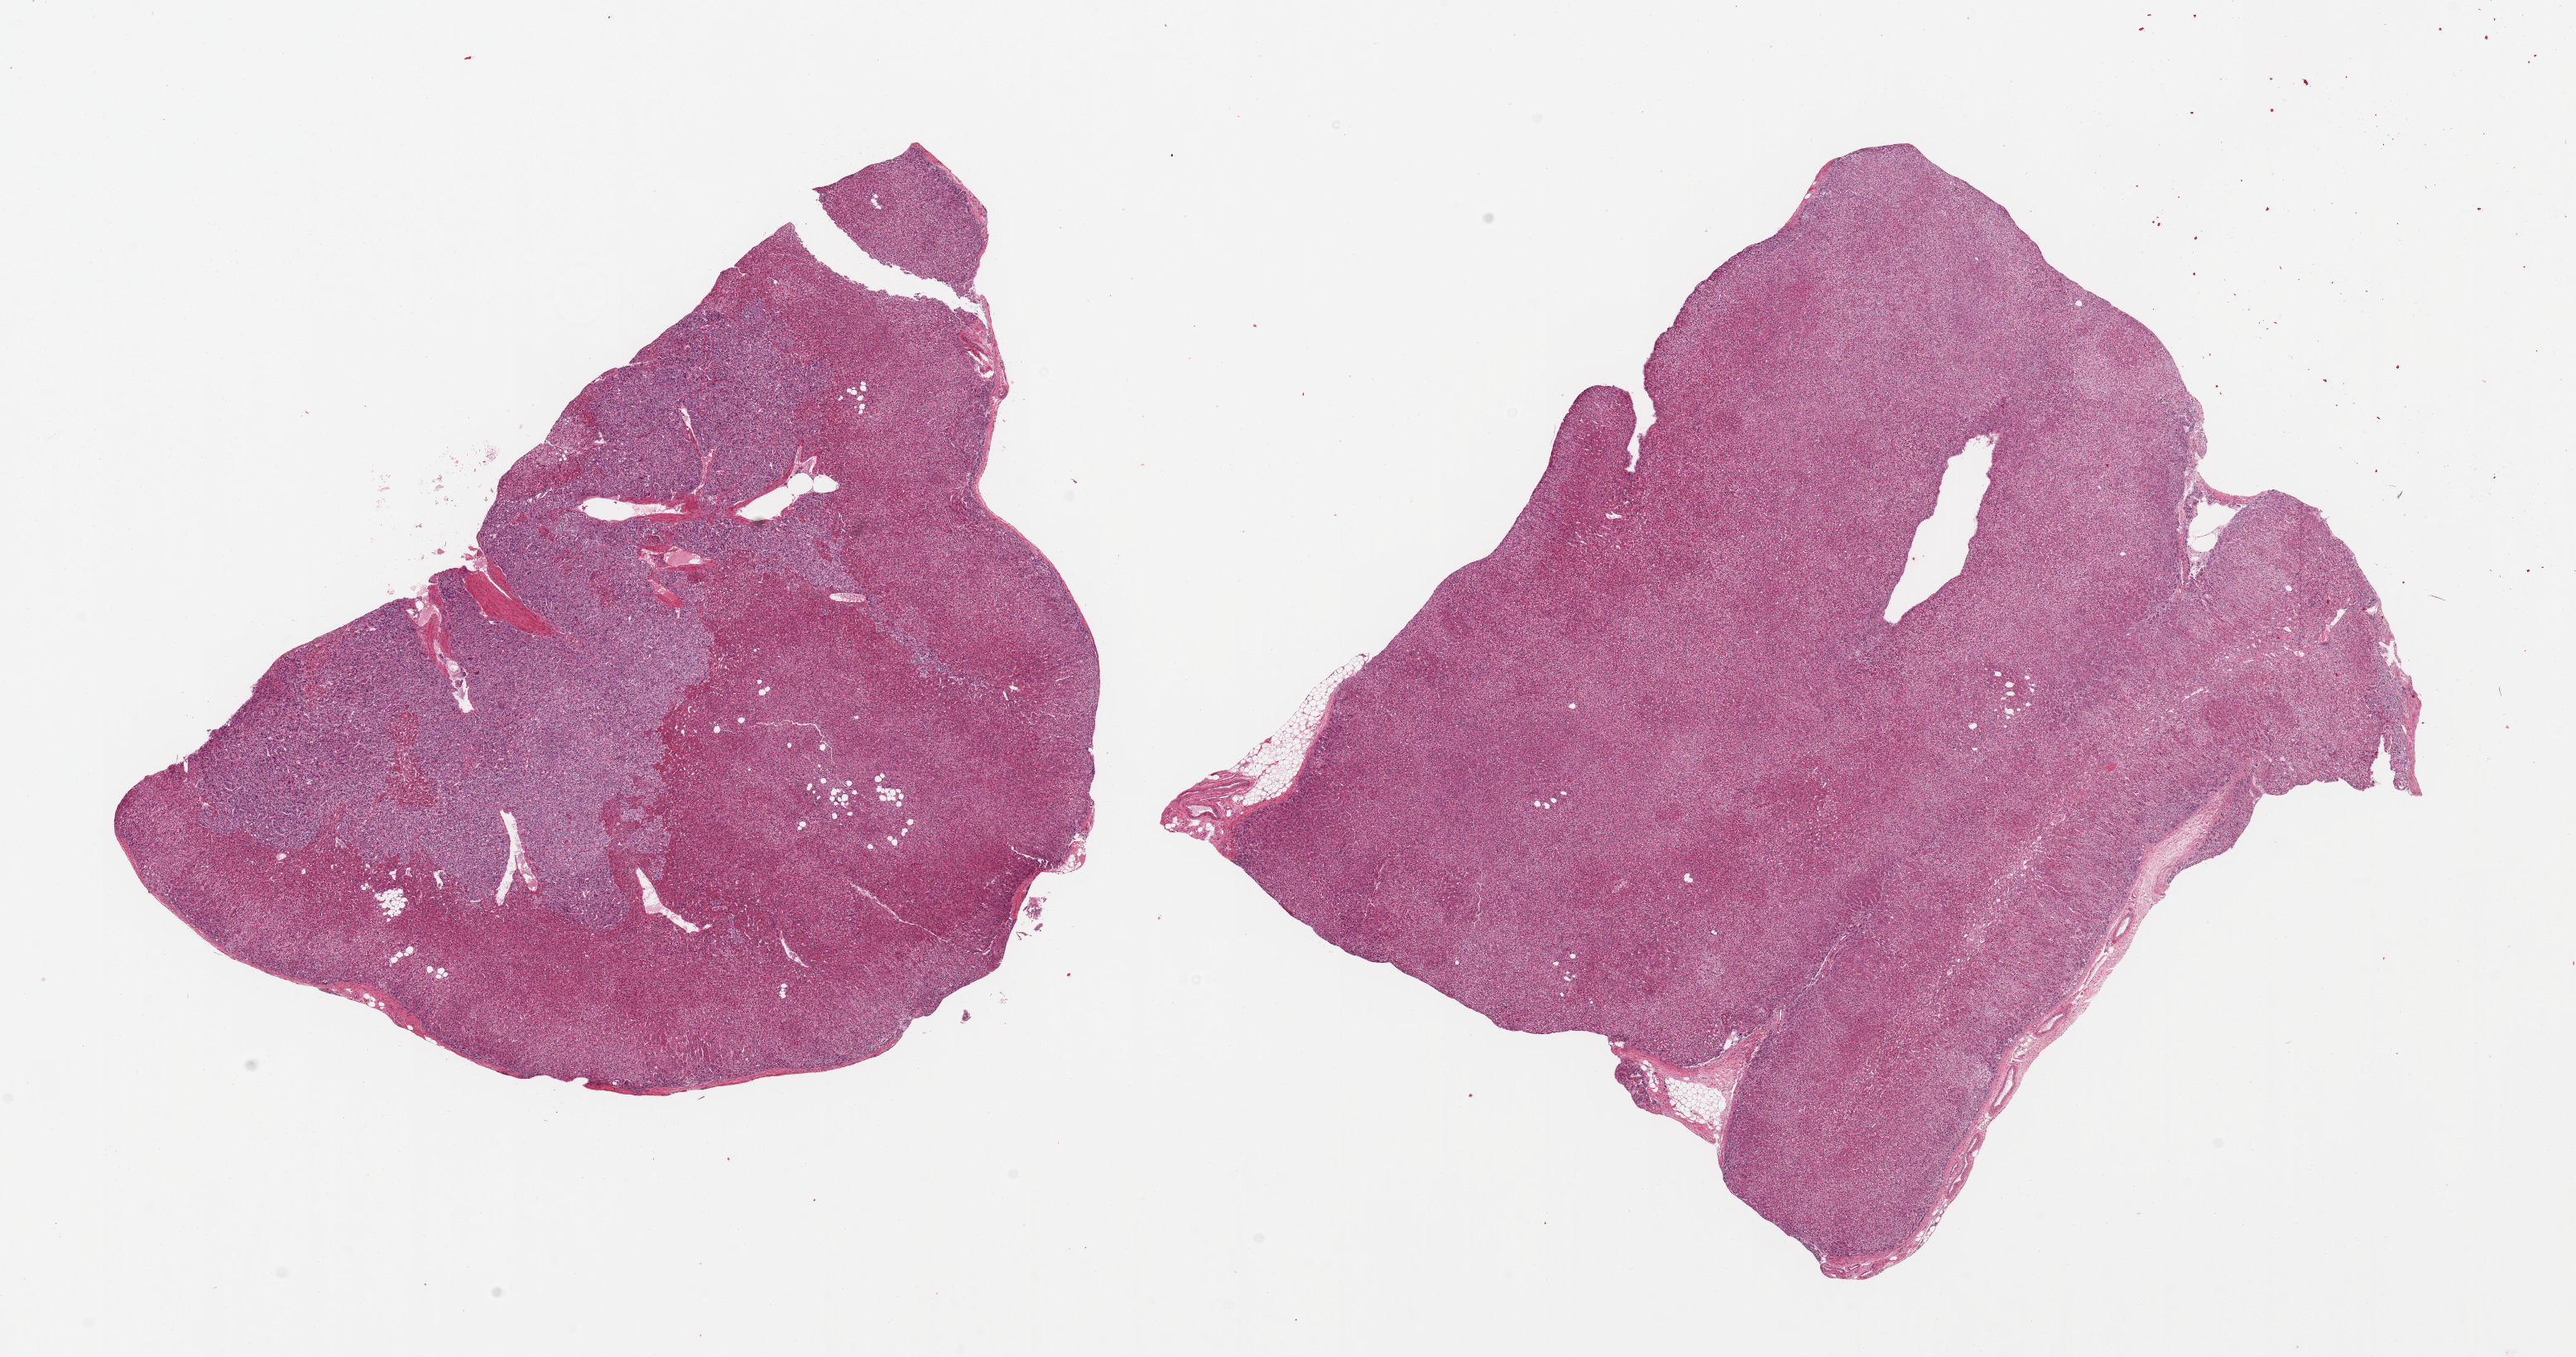
Digitized H&E-stained section — low-resolution overview of the scanned area, about 24.6 x 13.0 mm (slide scanned at 20x). PAXgene-fixed, paraffin-embedded tissue. Section of adrenal gland (target tissue). Donor tissue sample. Donor: female.
Pathologist's review note for this sample: 2 pieces; adrenal cortex and medulla.